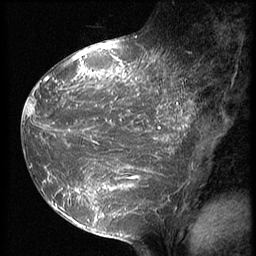
Breast MRI (dynamic contrast-enhanced), one sagittal slice; slice 26 of 64 in the series (ordered by position); 3 images stored at this slice position (order not interpretable as contrast timing); 1.5 T; TE 4.2 ms, TR 9 ms; 256 × 256 image matrix, field of view 180 × 180 mm. Female patient, age 39 years. Case-level facts recorded for this patient, not image findings: setting: breast cancer imaged before/during neoadjuvant chemotherapy; receptor status: HER2-positive.
Structures marked on this image (semi-automatic segmentation, software-assisted and operator-edited):
- analysis volume of interest (the breast-tissue region the enhancement analysis was run in; not a lesion): box from (x=23, y=47) to (x=194, y=239) px
- tumour enhancement mask (voxels above the 140 % enhancement threshold inside the analysis volume of interest): (x=23, y=47)–(x=194, y=228)